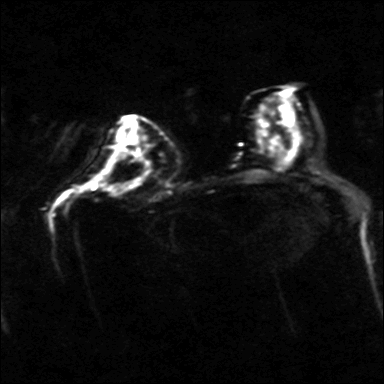
Breast MRI, one axial slice. Position 20 of 40 along the scan axis. Diffusion-weighted series; image 2 of 4 stored at this slice position (different b-values; order by instance number). 3 T. 384 × 384 image matrix, field of view 320 × 320 mm. Female patient.
Annotated regions visible in this slice (expert manual segmentation):
- tumour on diffusion-weighted imaging: bounding box [x1, y1, x2, y2] px = [125, 139, 131, 146]